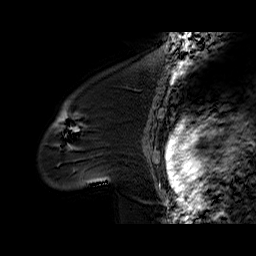
Breast MRI (dynamic contrast-enhanced), one sagittal slice; position 47 of 60 along the scan axis; dynamic contrast-enhanced series, time point 2 of 6 at this slice position (early post-contrast); 1.5 T; TE 6.2 ms, TR 32.4 ms; 4 mm slice thickness; 256 × 256 image matrix, field of view 200 × 200 mm. Female patient. Case-level facts recorded for this patient, not image findings: setting: breast cancer imaged before/during neoadjuvant chemotherapy; receptor status: triple-negative.
Structures marked on this image (semi-automatically segmented with operator editing):
- analysis volume of interest (the breast-tissue region the enhancement analysis was run in; not a lesion): bounding box (x1, y1, x2, y2) in pixels: (39, 97, 134, 189)
- tumour enhancement mask (voxels above the 100 % enhancement threshold inside the analysis volume of interest): (59, 103, 77, 149)